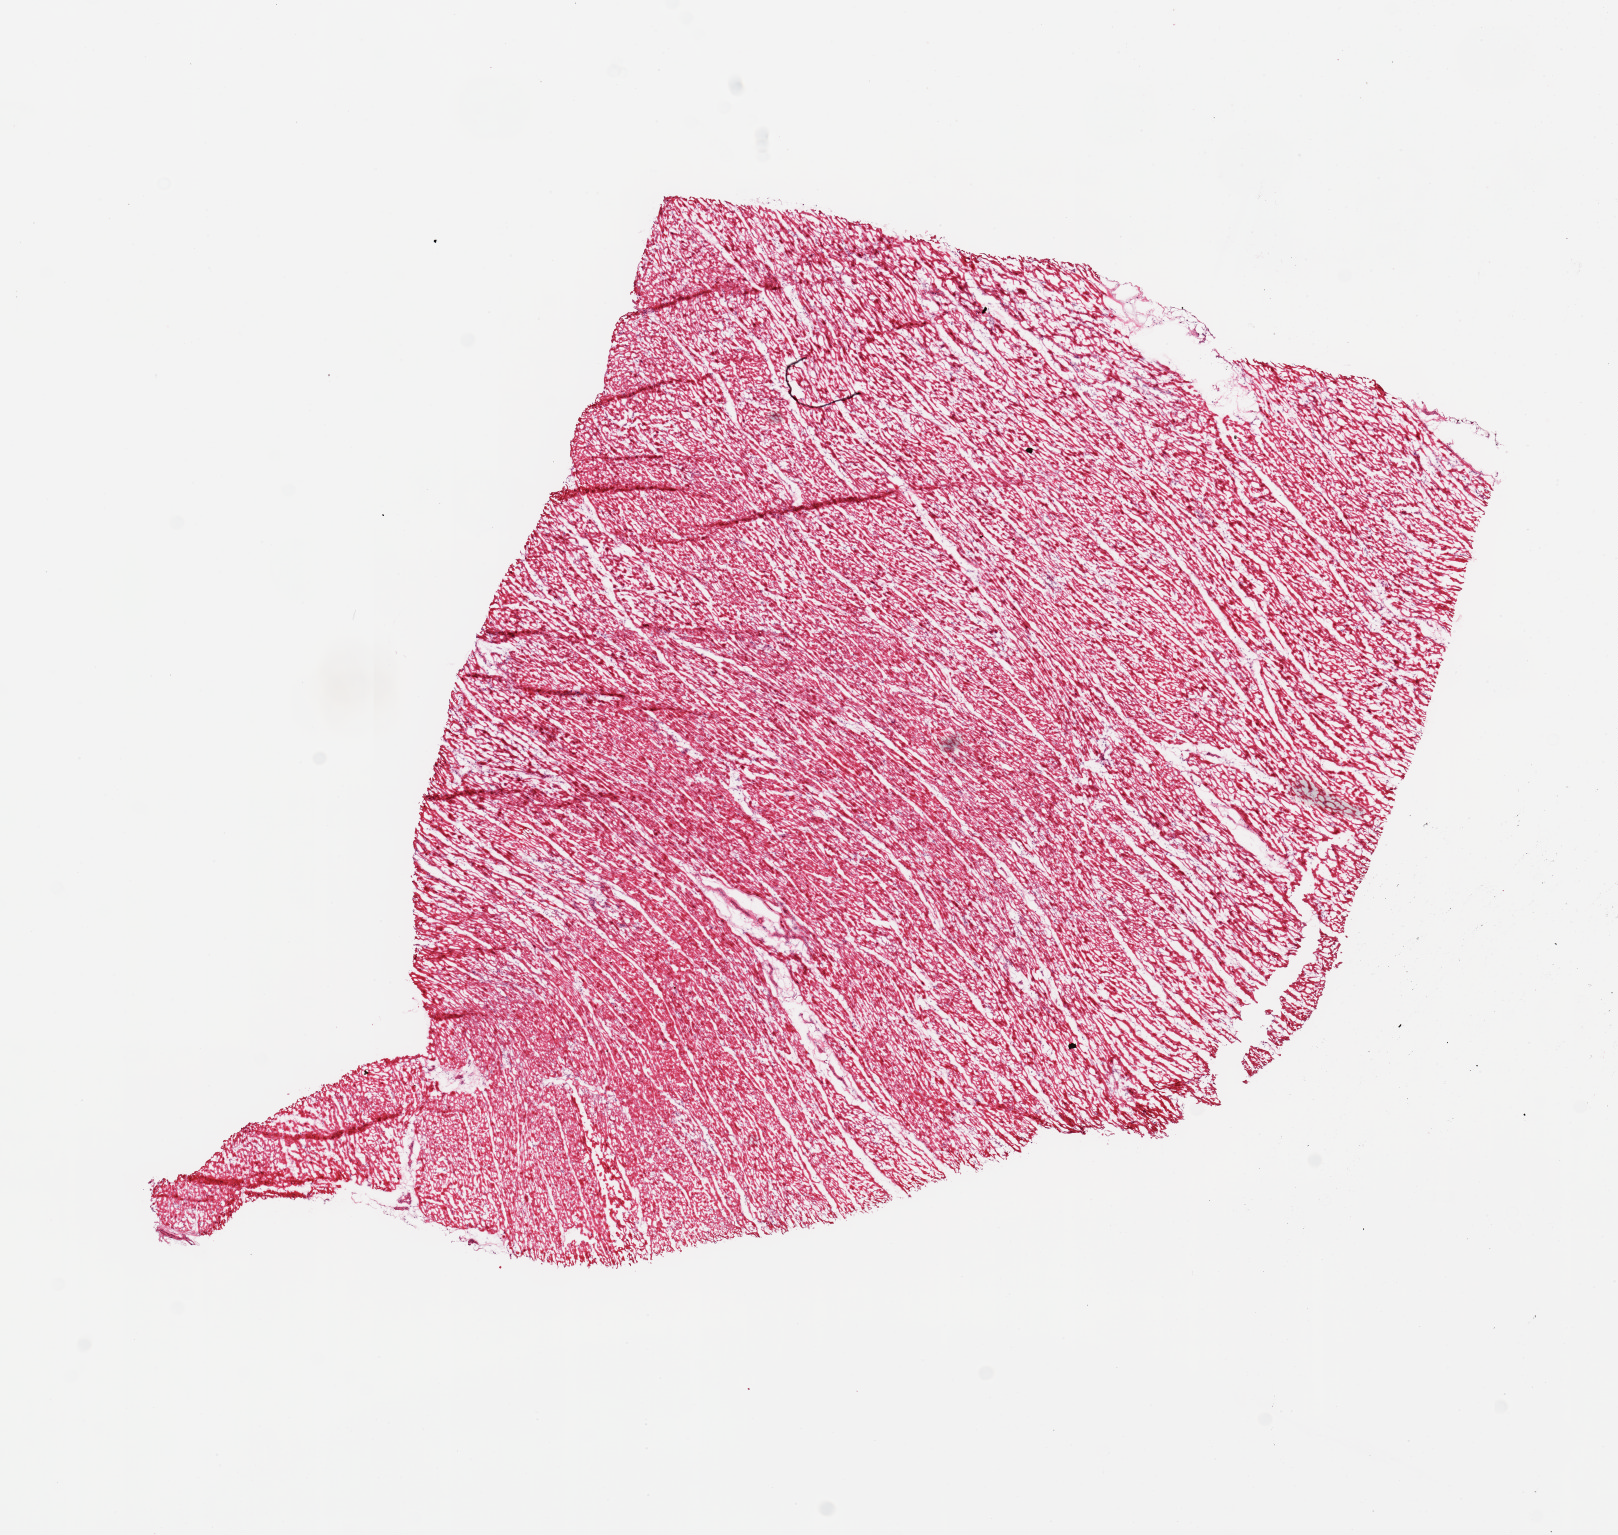
Hematoxylin and eosin (H&E) whole-slide image — whole scanned area (about 12.8 x 12.1 mm, from a 20x scan) shown as a low-resolution overview; frozen section (dry ice); target tissue: heart; tissue donor sample. Donor sex: female.
• review note (as recorded): 1 piece